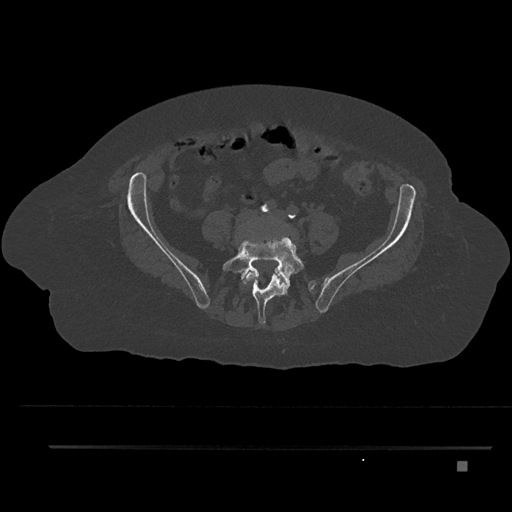
CT including the spine, one axial slice; slice 45 of 797 in the series (ordered by position); 120 kVp; bone window (W 1800 / L 400 HU); 0.5 mm slice thickness; 512 × 512 image matrix, field of view 437 × 437 mm. Female patient, age 76 years. Case-level facts recorded for this patient, not image findings: primary cancer: lung.
Structures marked on this image (semi-automatic segmentation, software-assisted and operator-edited):
- L4 vertebra: bounding box (x1, y1, x2, y2) in pixels: (244, 268, 287, 303)
- L5 vertebra: (222, 226, 305, 324)